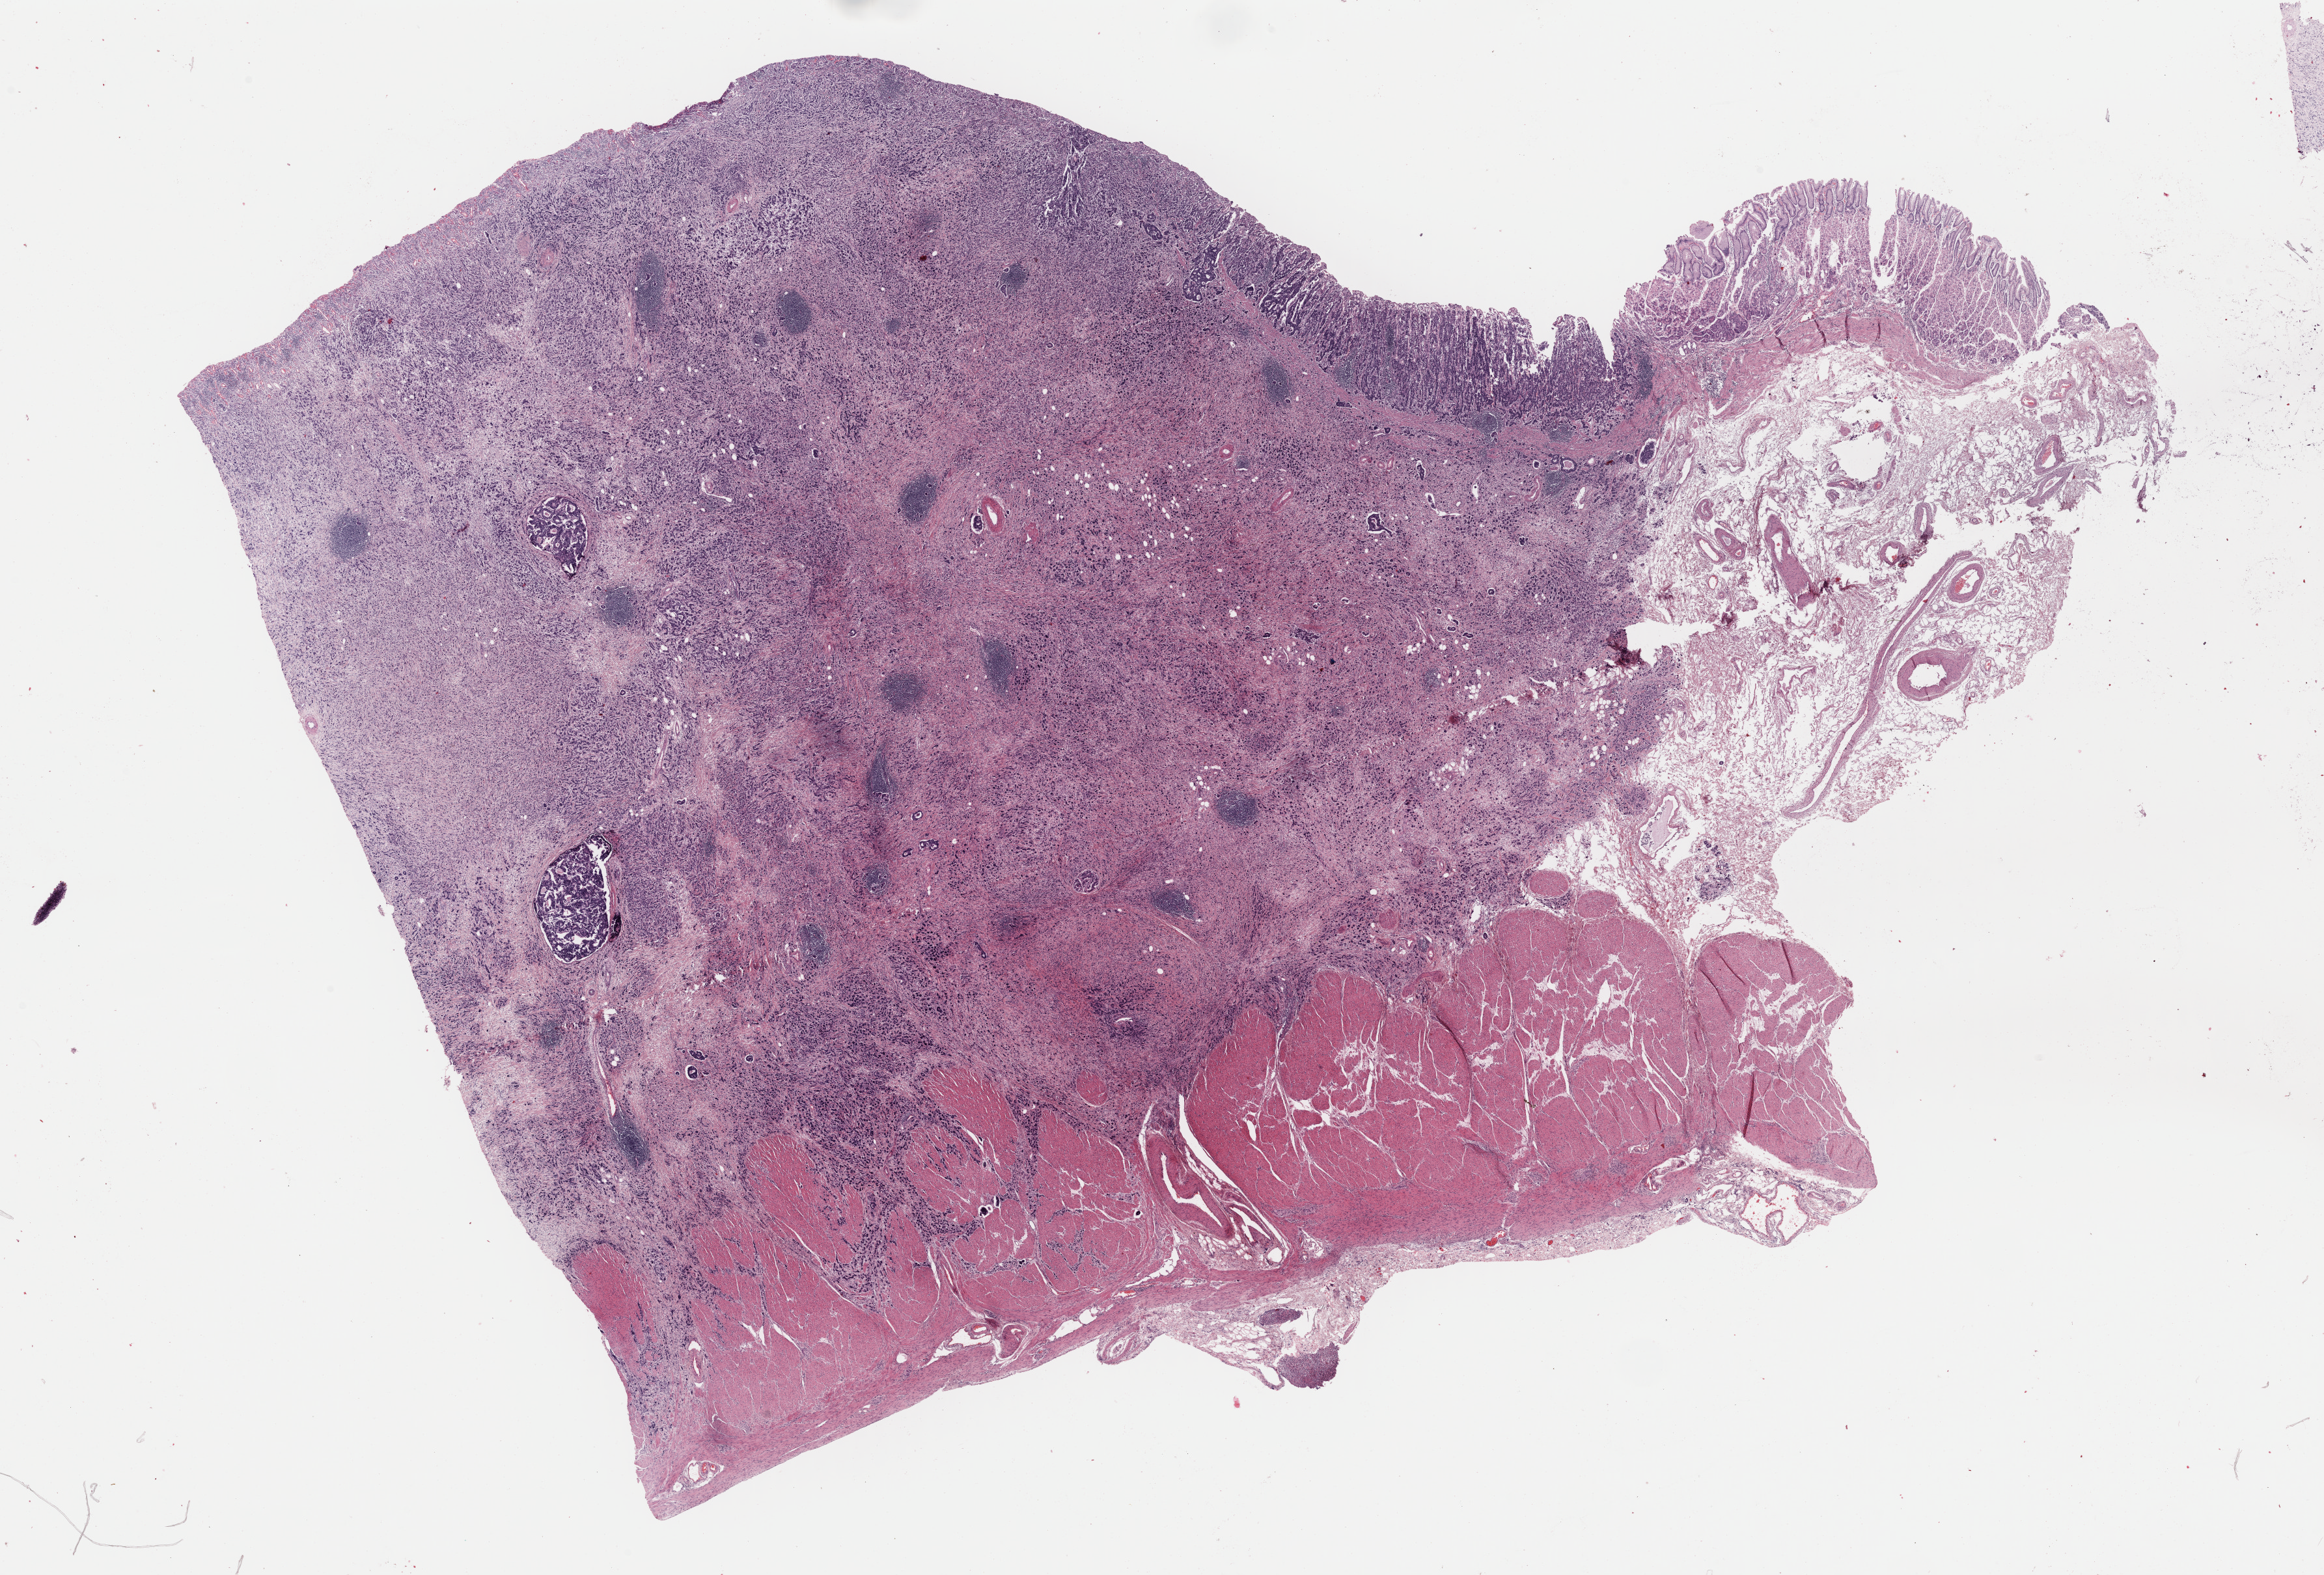
H&E whole-slide image — low-resolution overview of the scanned area, about 28.2 x 19.1 mm (slide scanned at 40x), formalin-fixed paraffin-embedded (FFPE) diagnostic section, primary tumour sample from the stomach. Male, age 73 years at initial diagnosis. Histologic grade: G3 (poorly differentiated).
AJCC pathologic stage: IIIB (7th edition). Pathologic diagnosis: Tubular adenocarcinoma (fundus of stomach).